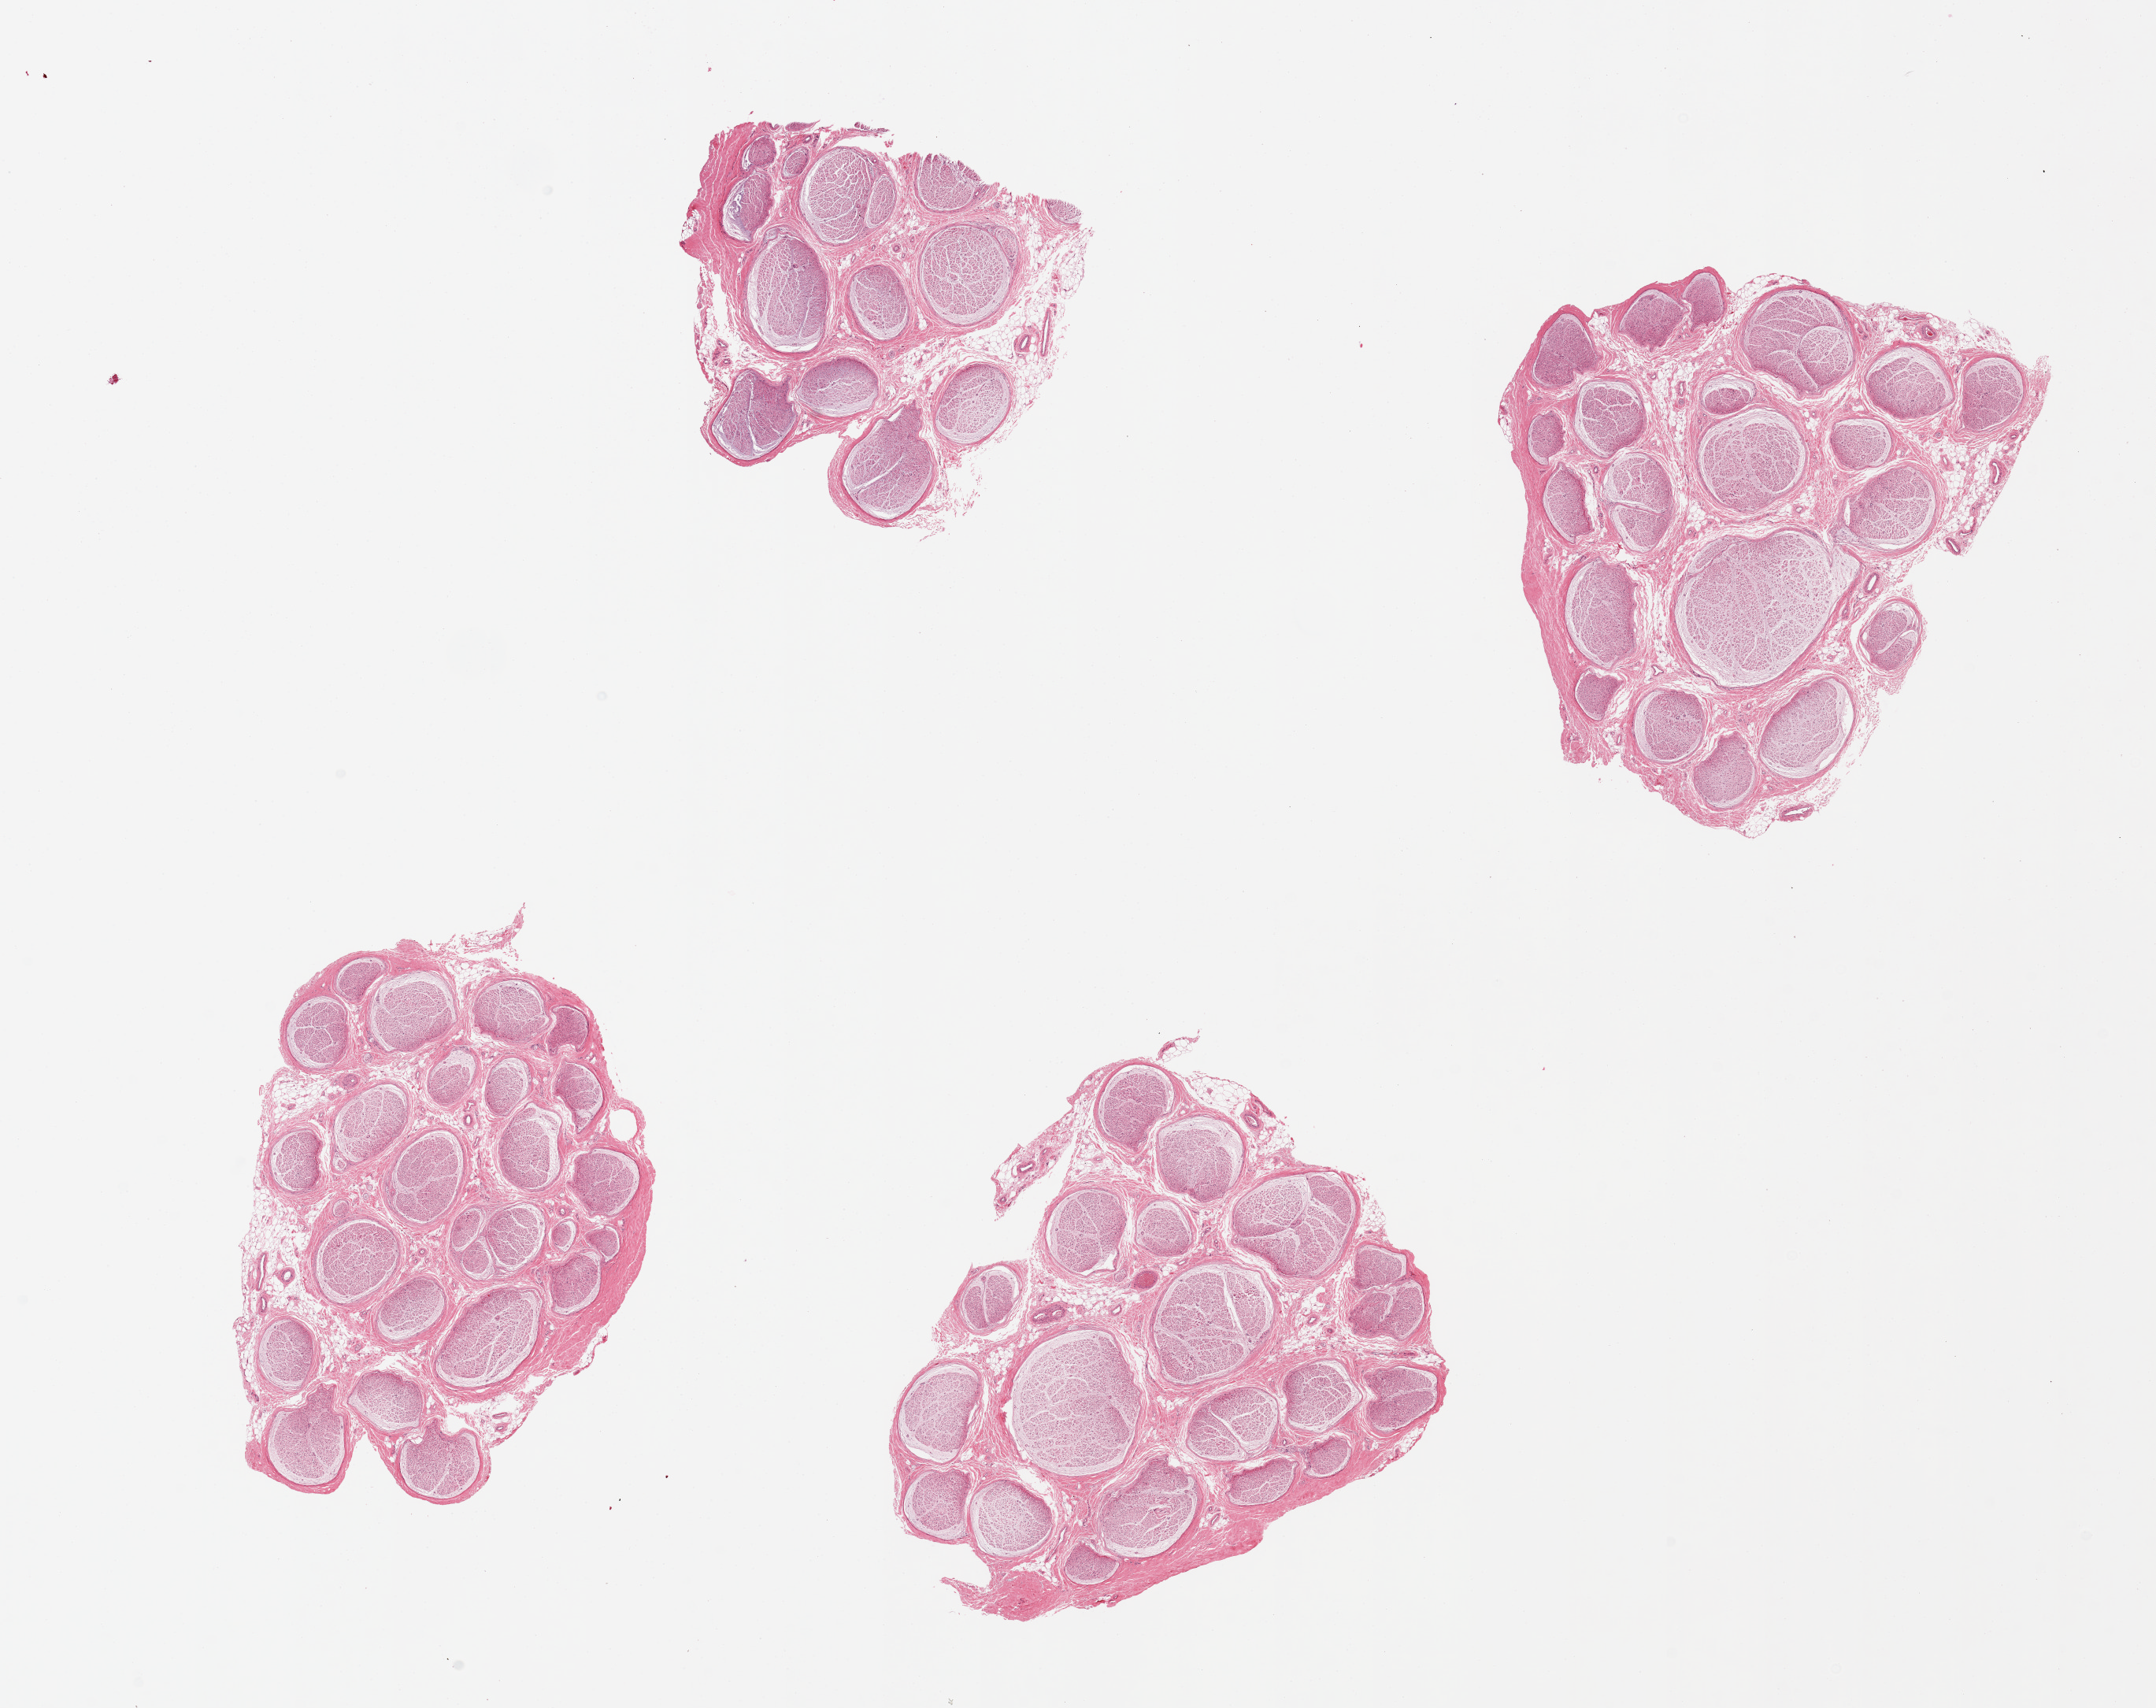
Digitized H&E-stained section, whole scanned area (about 21.7 x 17.2 mm, slide scanned at 20x) shown as a low-resolution overview. PAXgene-fixed, paraffin-embedded tissue. Sampled site (target tissue): tibial nerve. Tissue donor sample. Donor sex: male.
* reviewer comment on this tissue sample: 4 pieces. Well trimmed